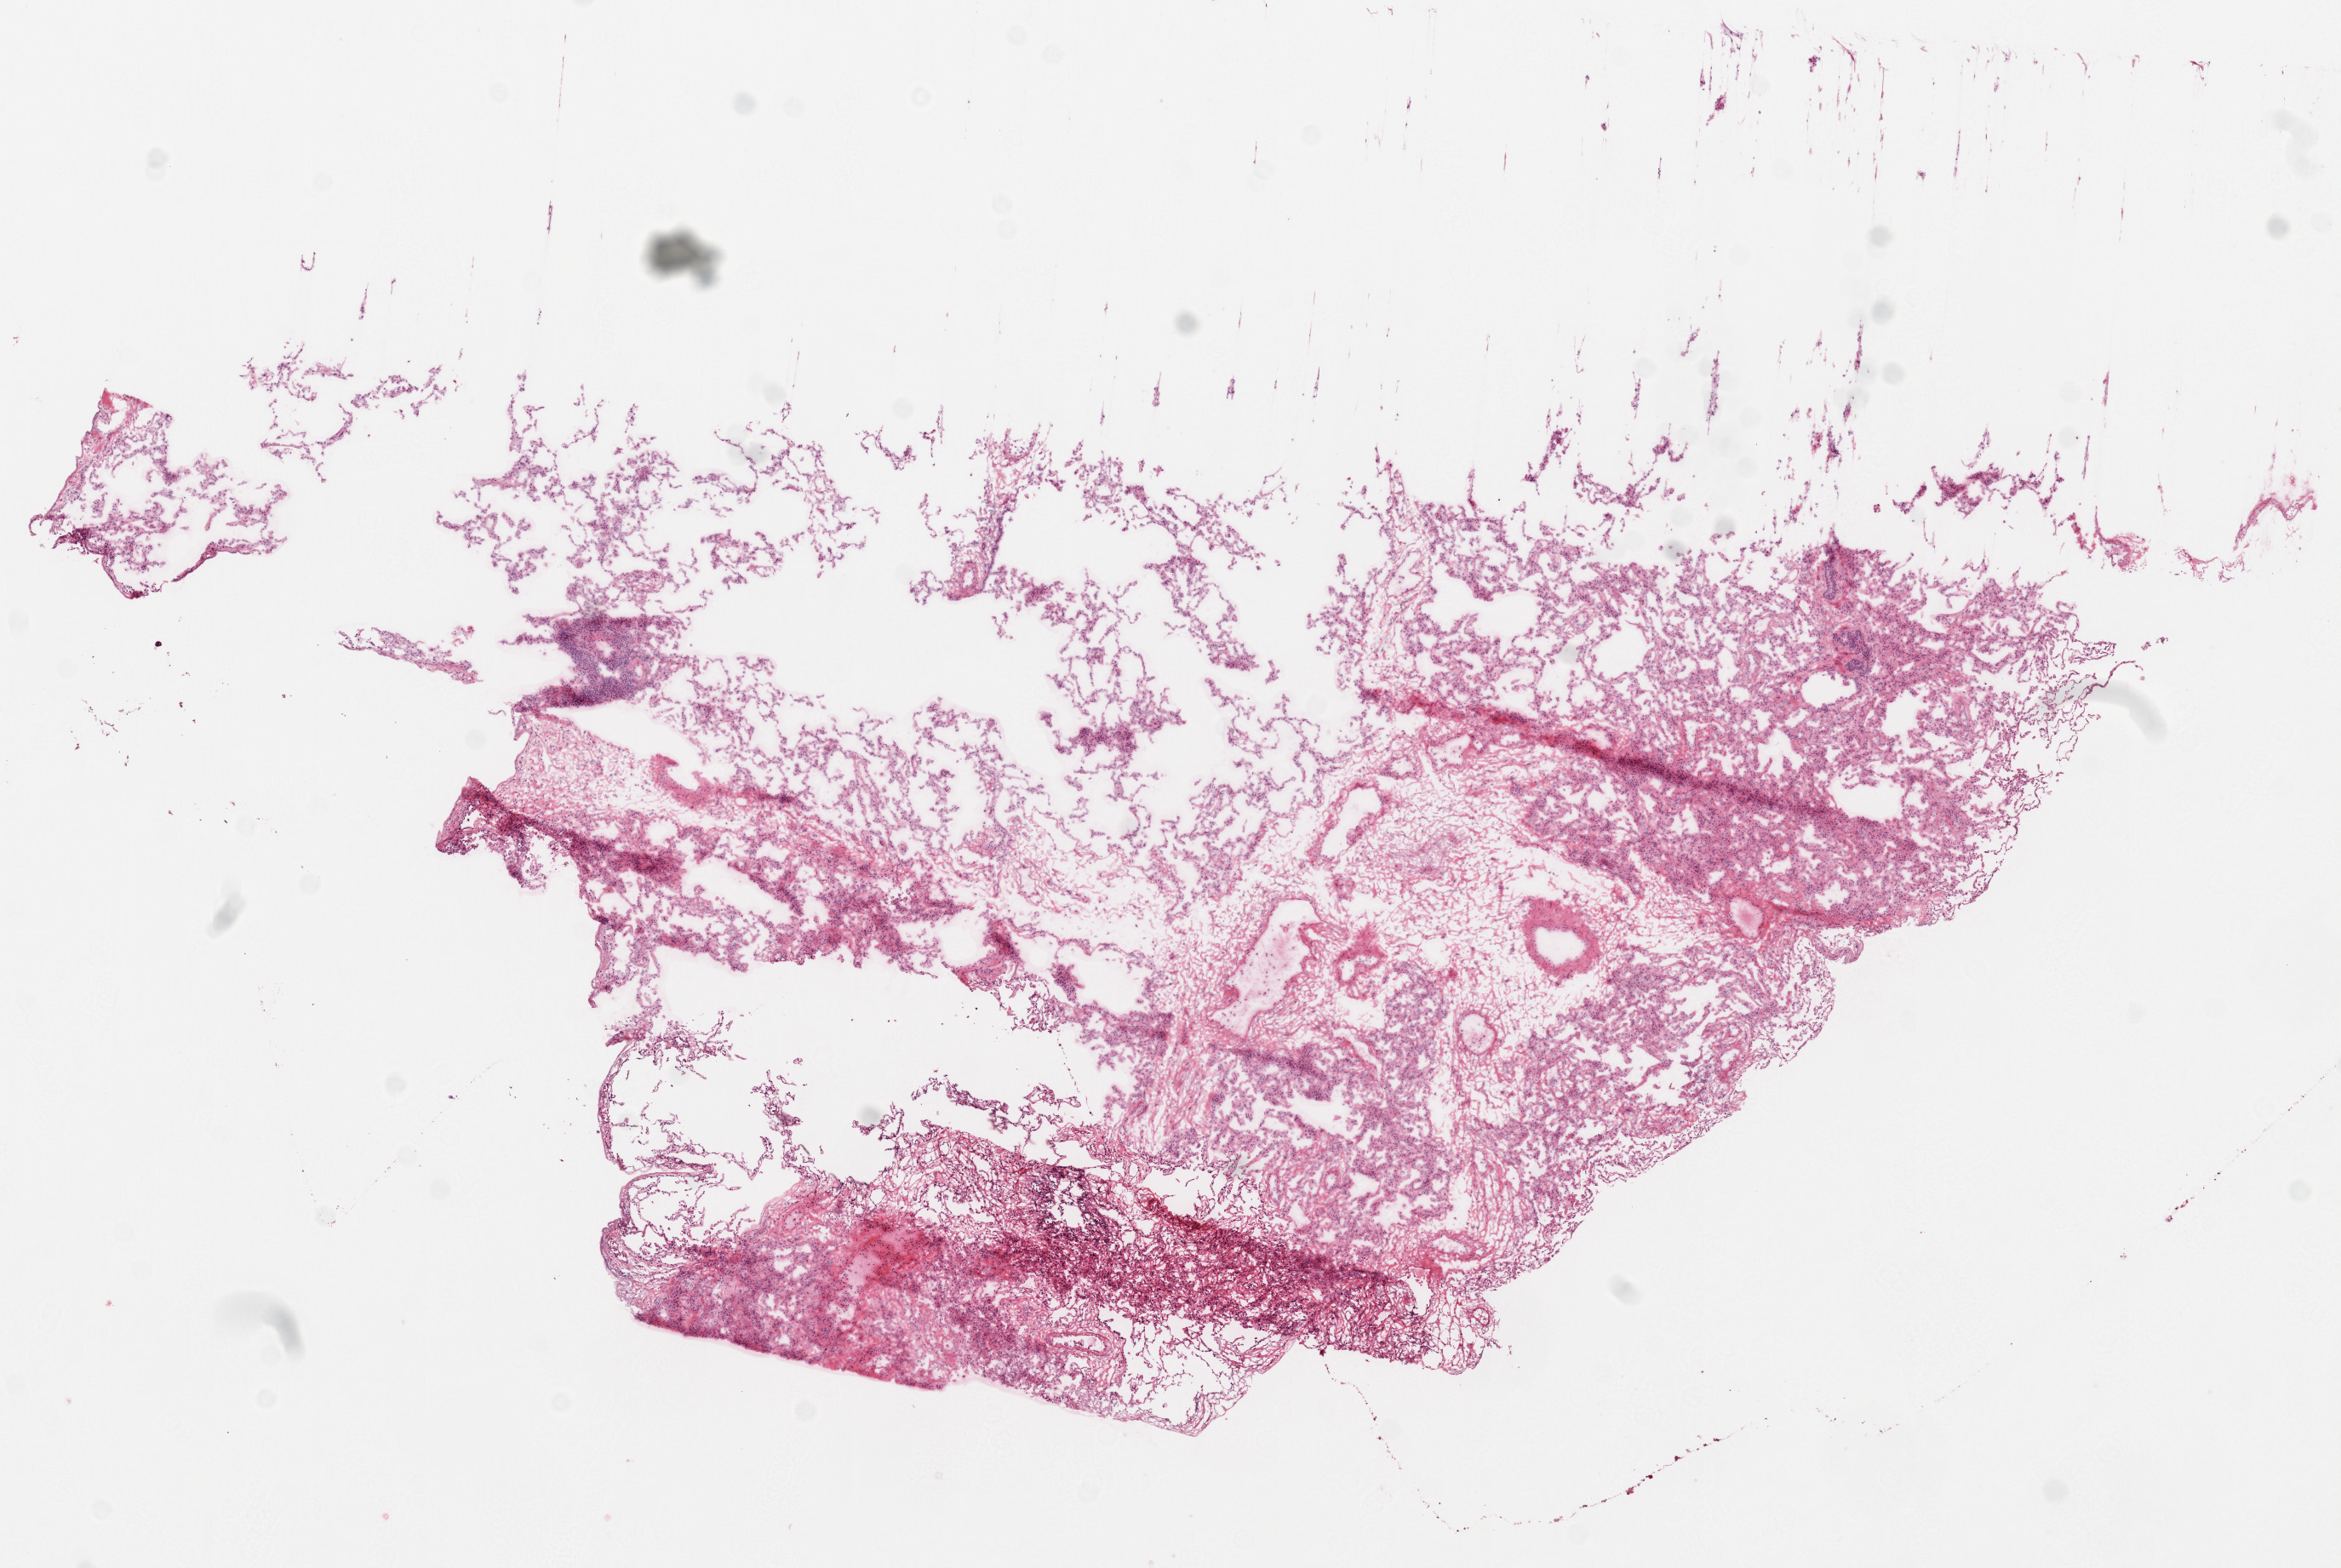
Hematoxylin and eosin (H&E) stained whole-slide image, a low-resolution overview of the entire scanned area, about 11.0 x 7.4 mm (slide scanned at 20x), frozen section from the top of the tissue portion, lung, solid tissue normal (non-tumour tissue) sample. Female patient; age at initial diagnosis 60 years.
This section: solid tissue normal sample (biorepository sample class). Patient diagnosis: Squamous cell carcinoma, NOS (upper lobe, lung).